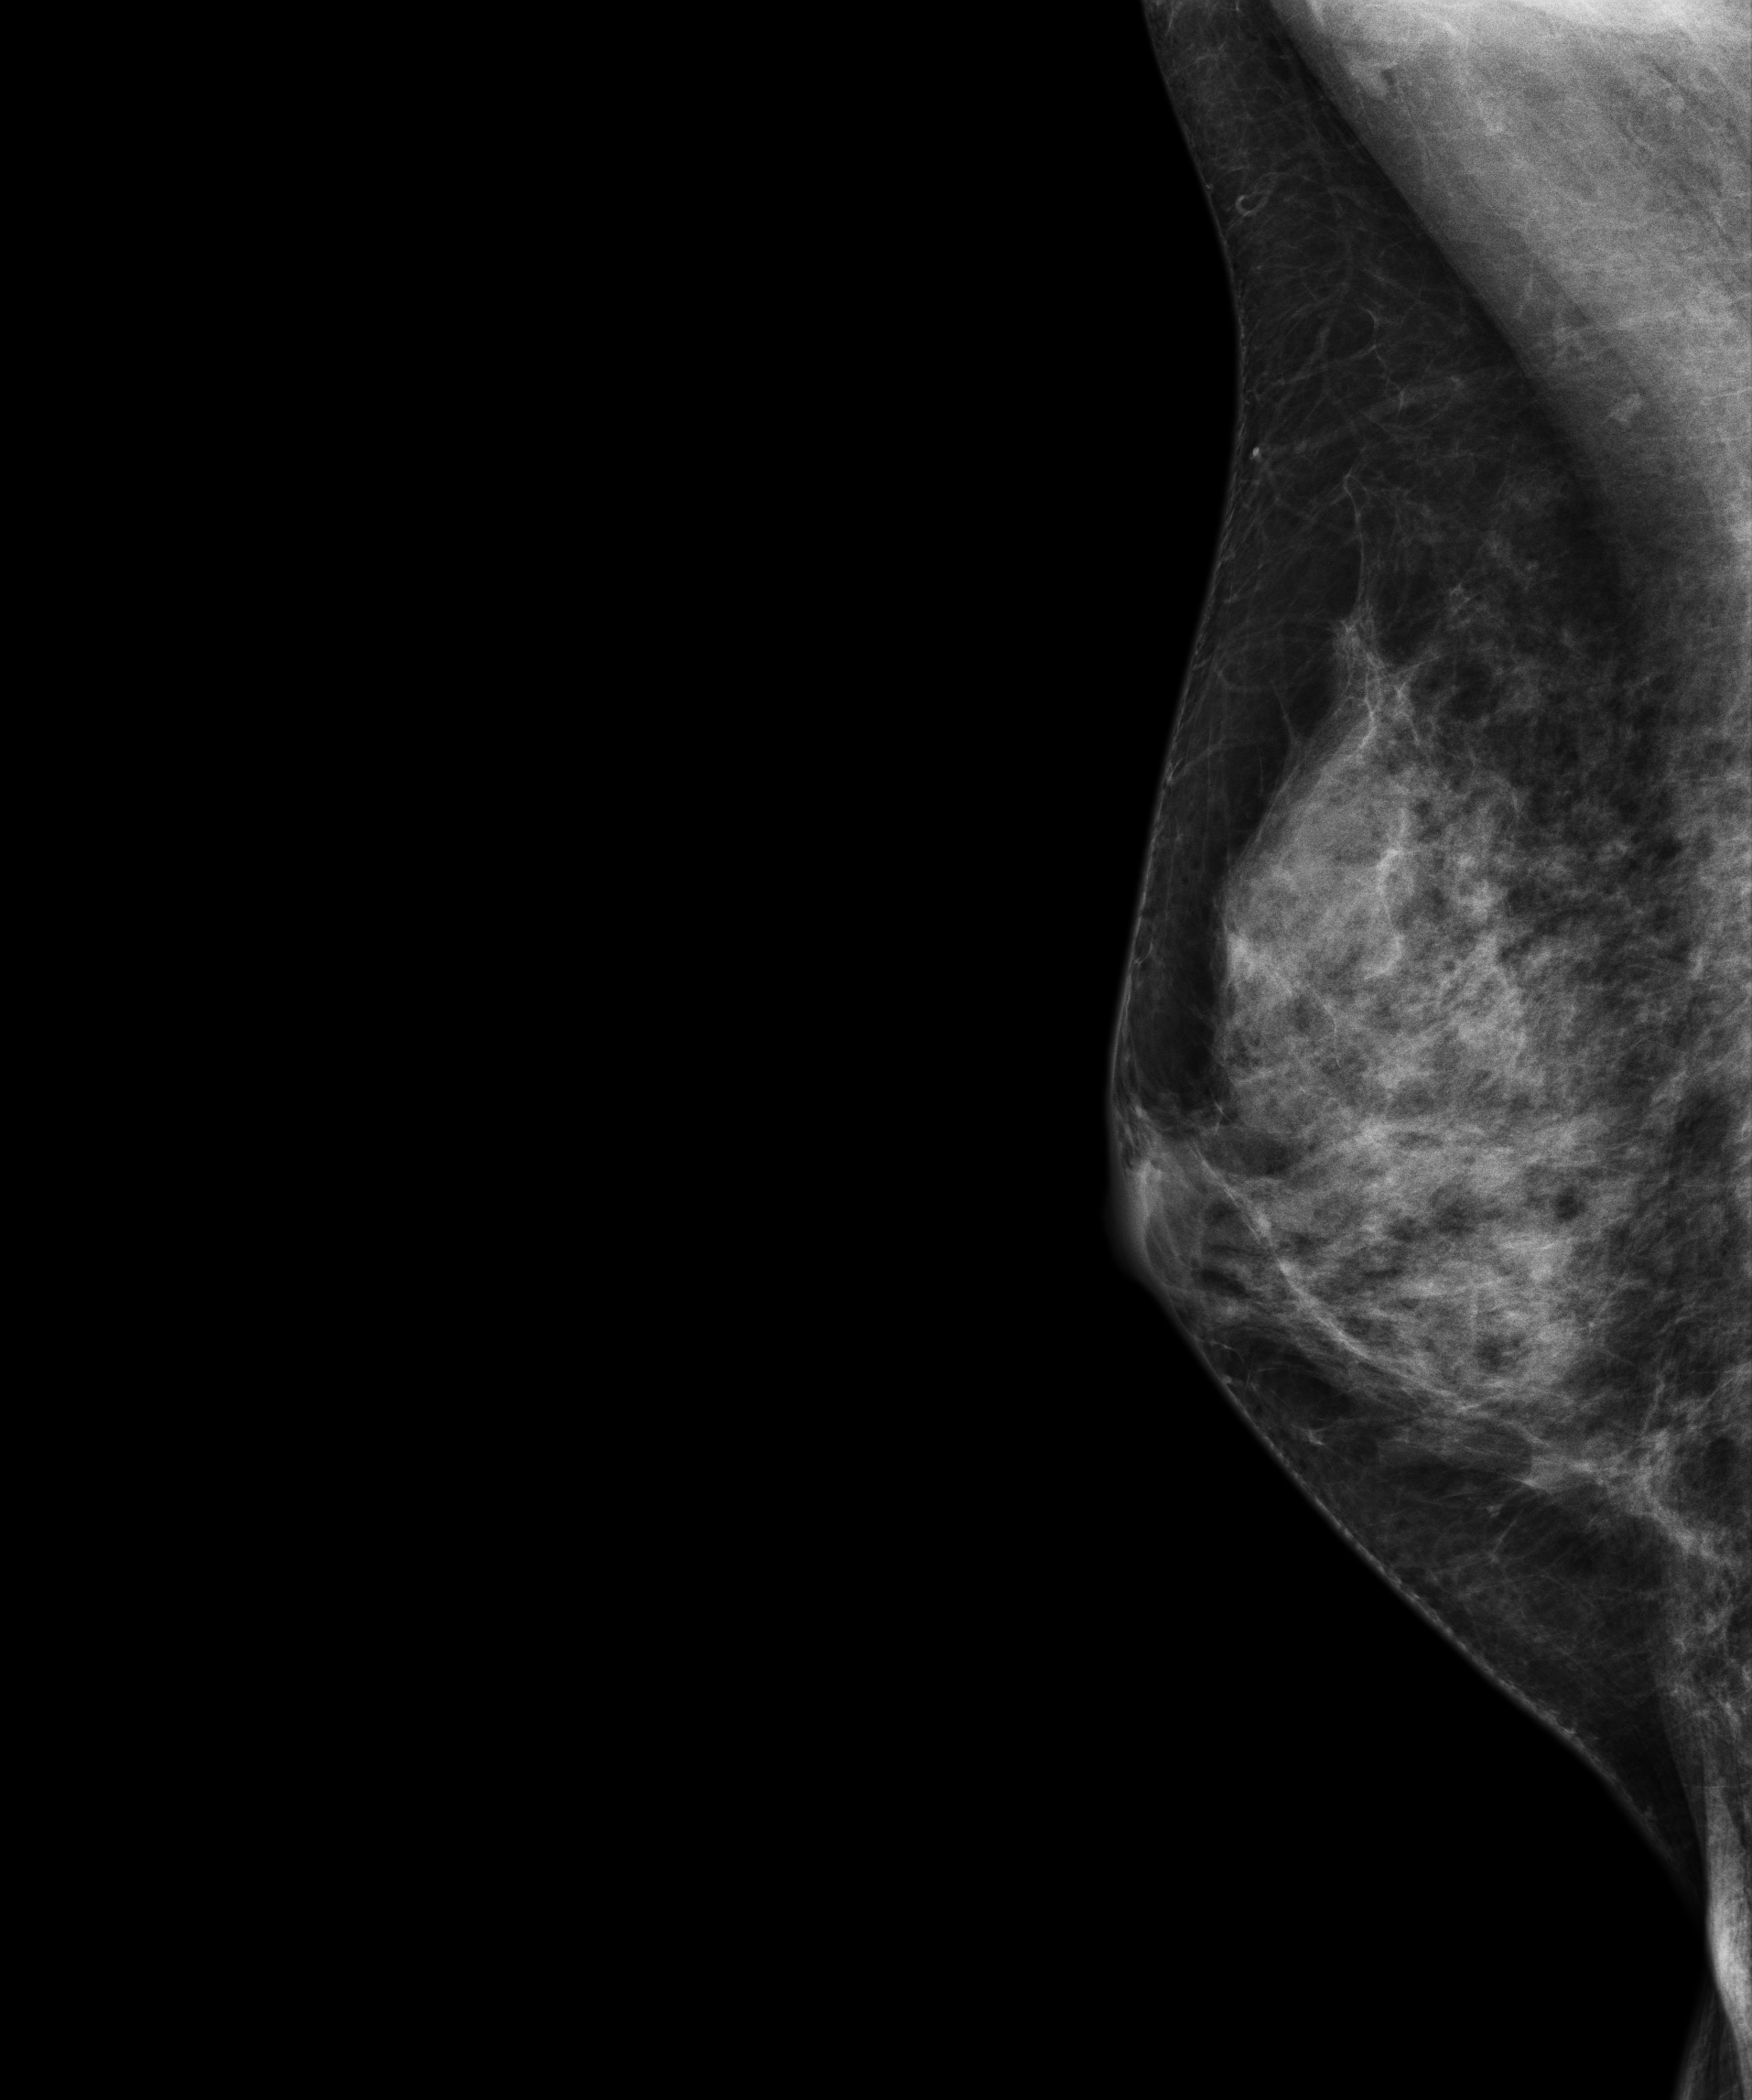
Annual screening mammography examination. Patient aged 56 years (female).
Image type: full-field digital mammogram. Breast: right. Projection: medio-lateral oblique projection.